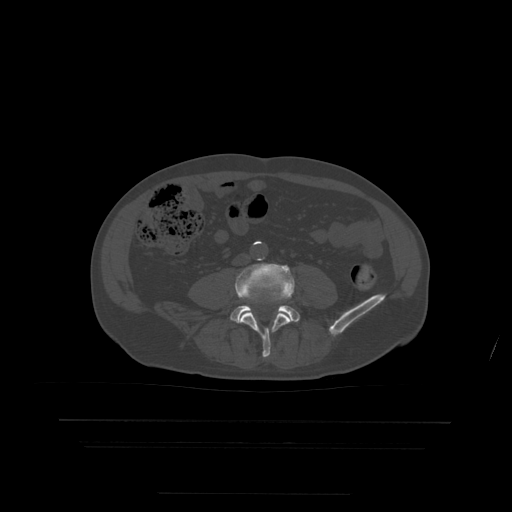
CT including the spine, one axial slice; slice 87 of 522 in the series (ordered by position); bone window (W 1800 / L 400 HU); 1.25 mm slice thickness; 512 × 512 image matrix, field of view 436 × 436 mm. Patient age 68 years. From the clinical record (not read from this slice): primary cancer: urothelial.
Outlined on this slice (semi-automatically segmented with operator editing):
- L4 vertebra: bounding box [x1, y1, x2, y2] px = [236, 264, 295, 358]
- L5 vertebra: [231, 298, 300, 323]